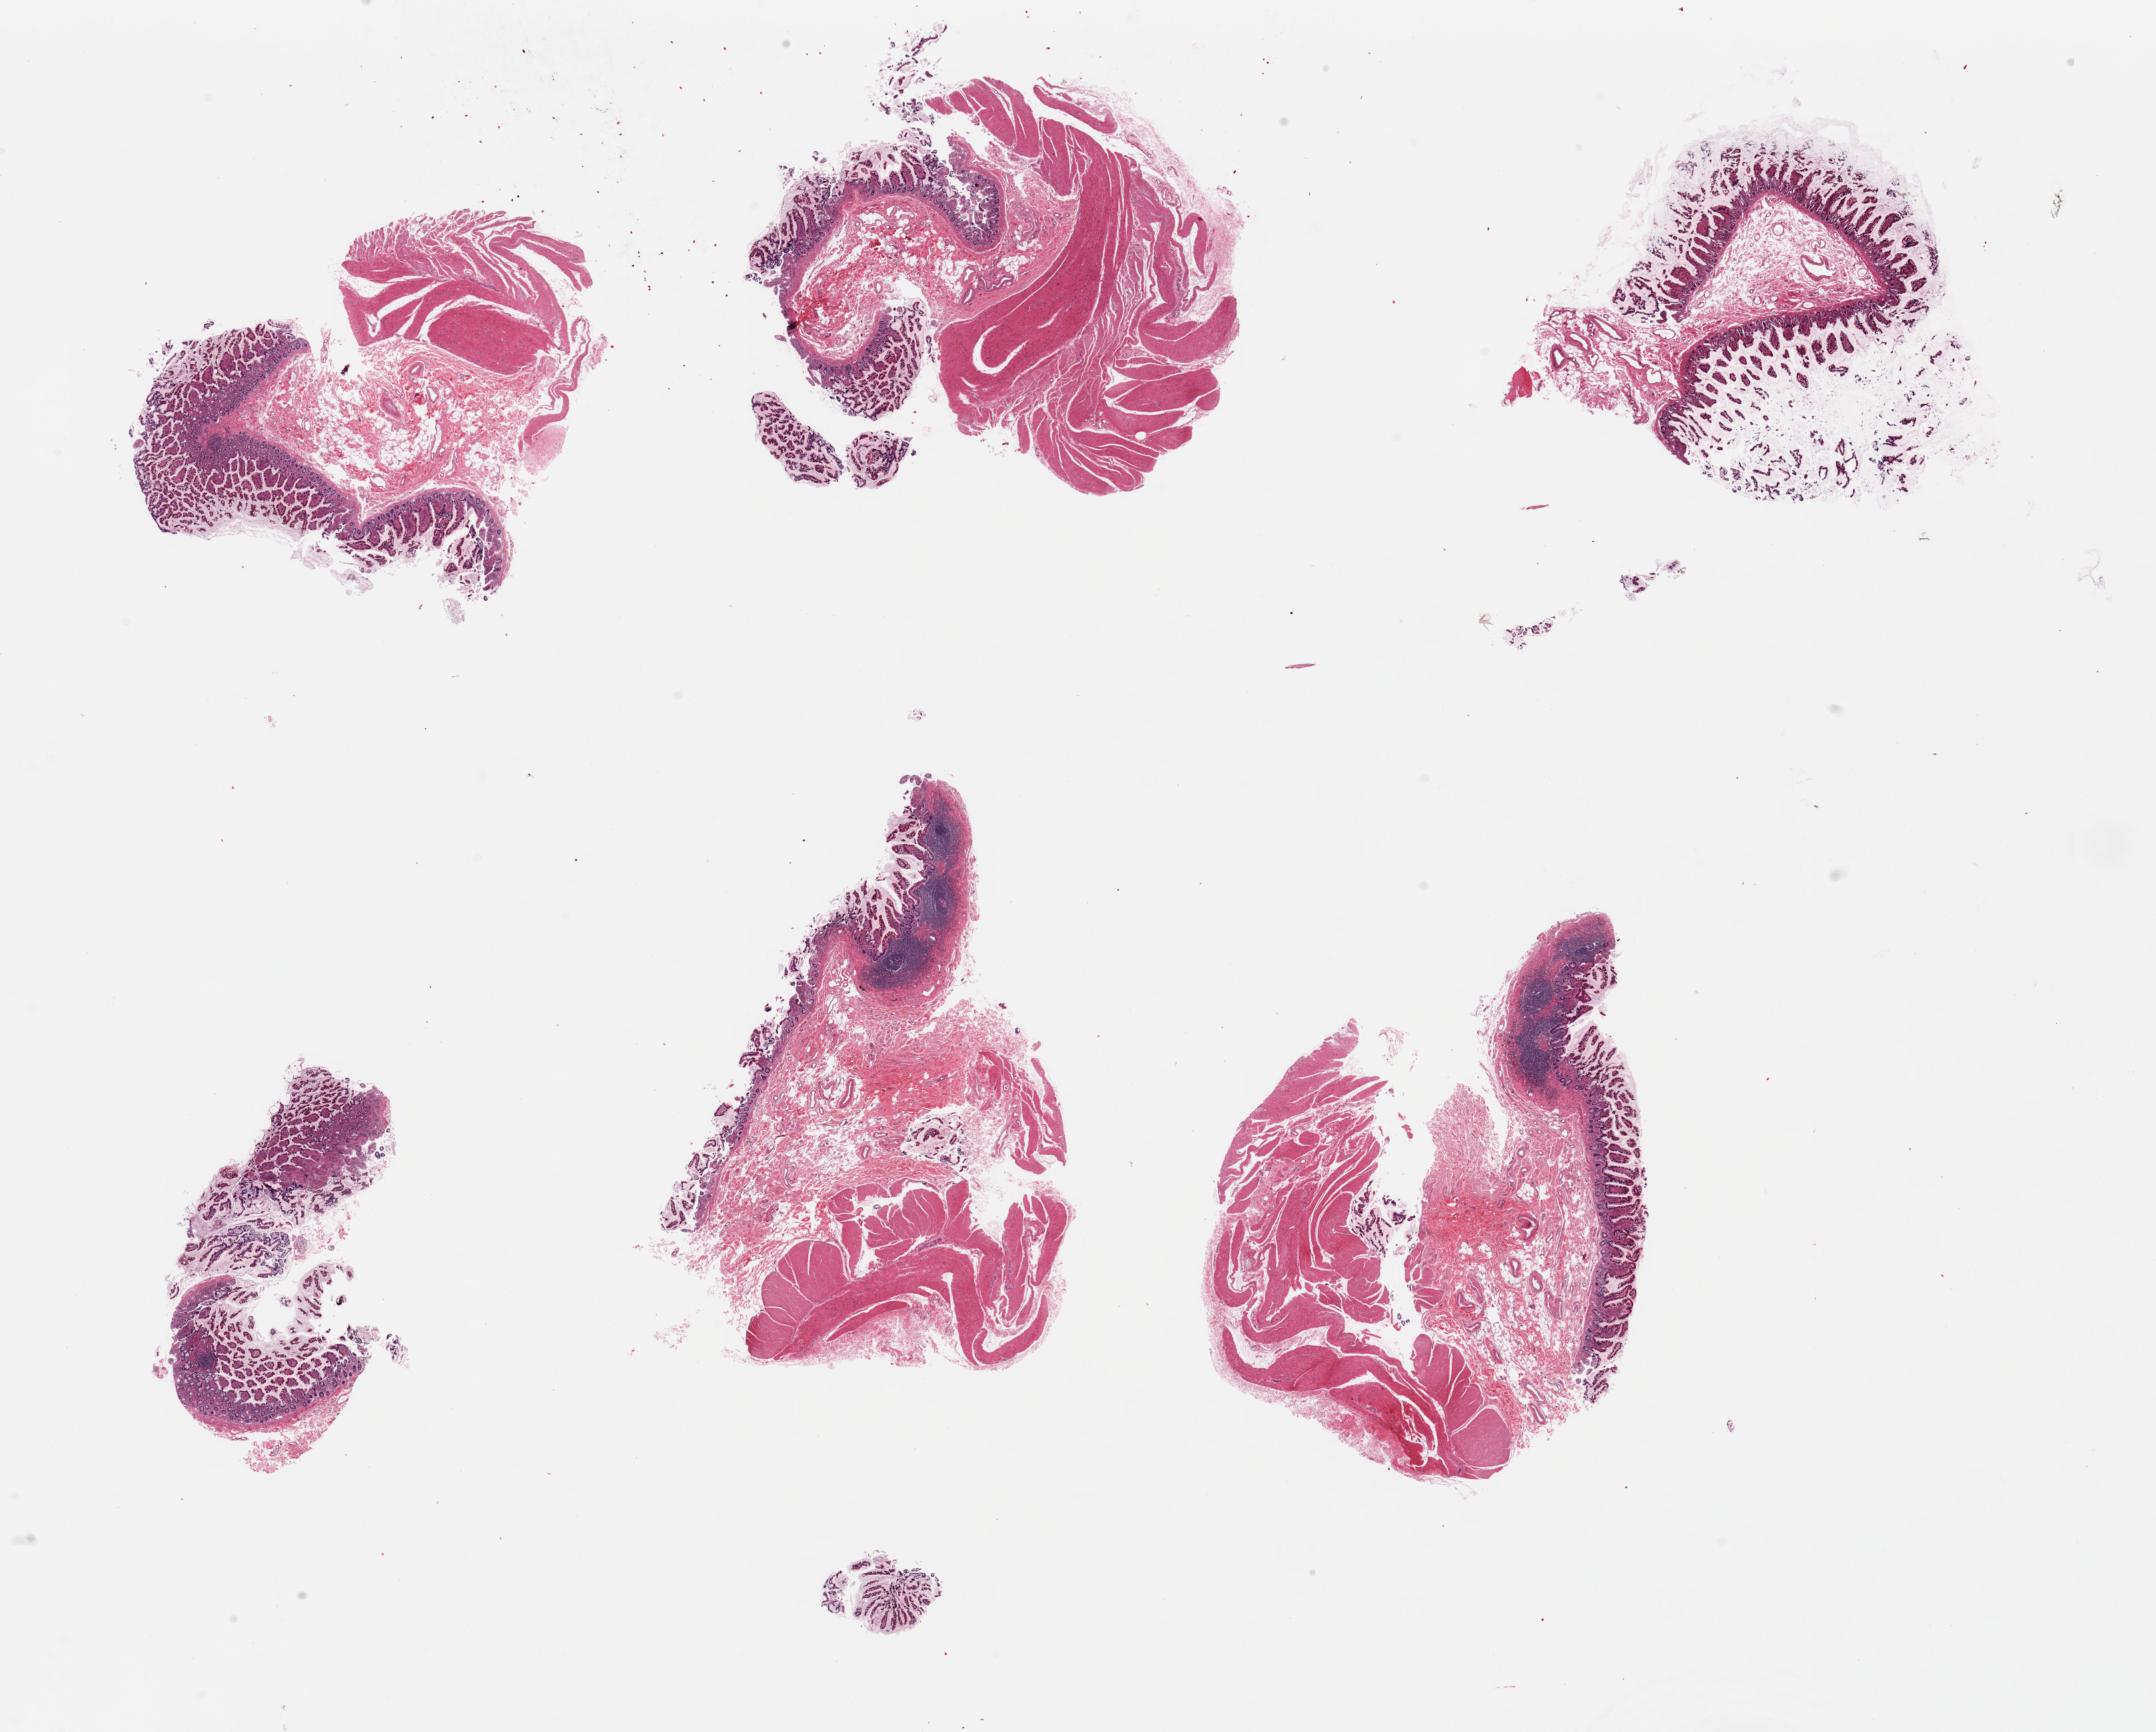
Hematoxylin and eosin (H&E) whole-slide image, brightfield, a low-resolution overview of the entire scanned area, about 25.6 x 20.6 mm (slide scanned at 20x). Donor: male.
Specimen: PAXgene-fixed paraffin-embedded (PFPE) section; sampled site (target tissue): ileum; donor tissue sample.